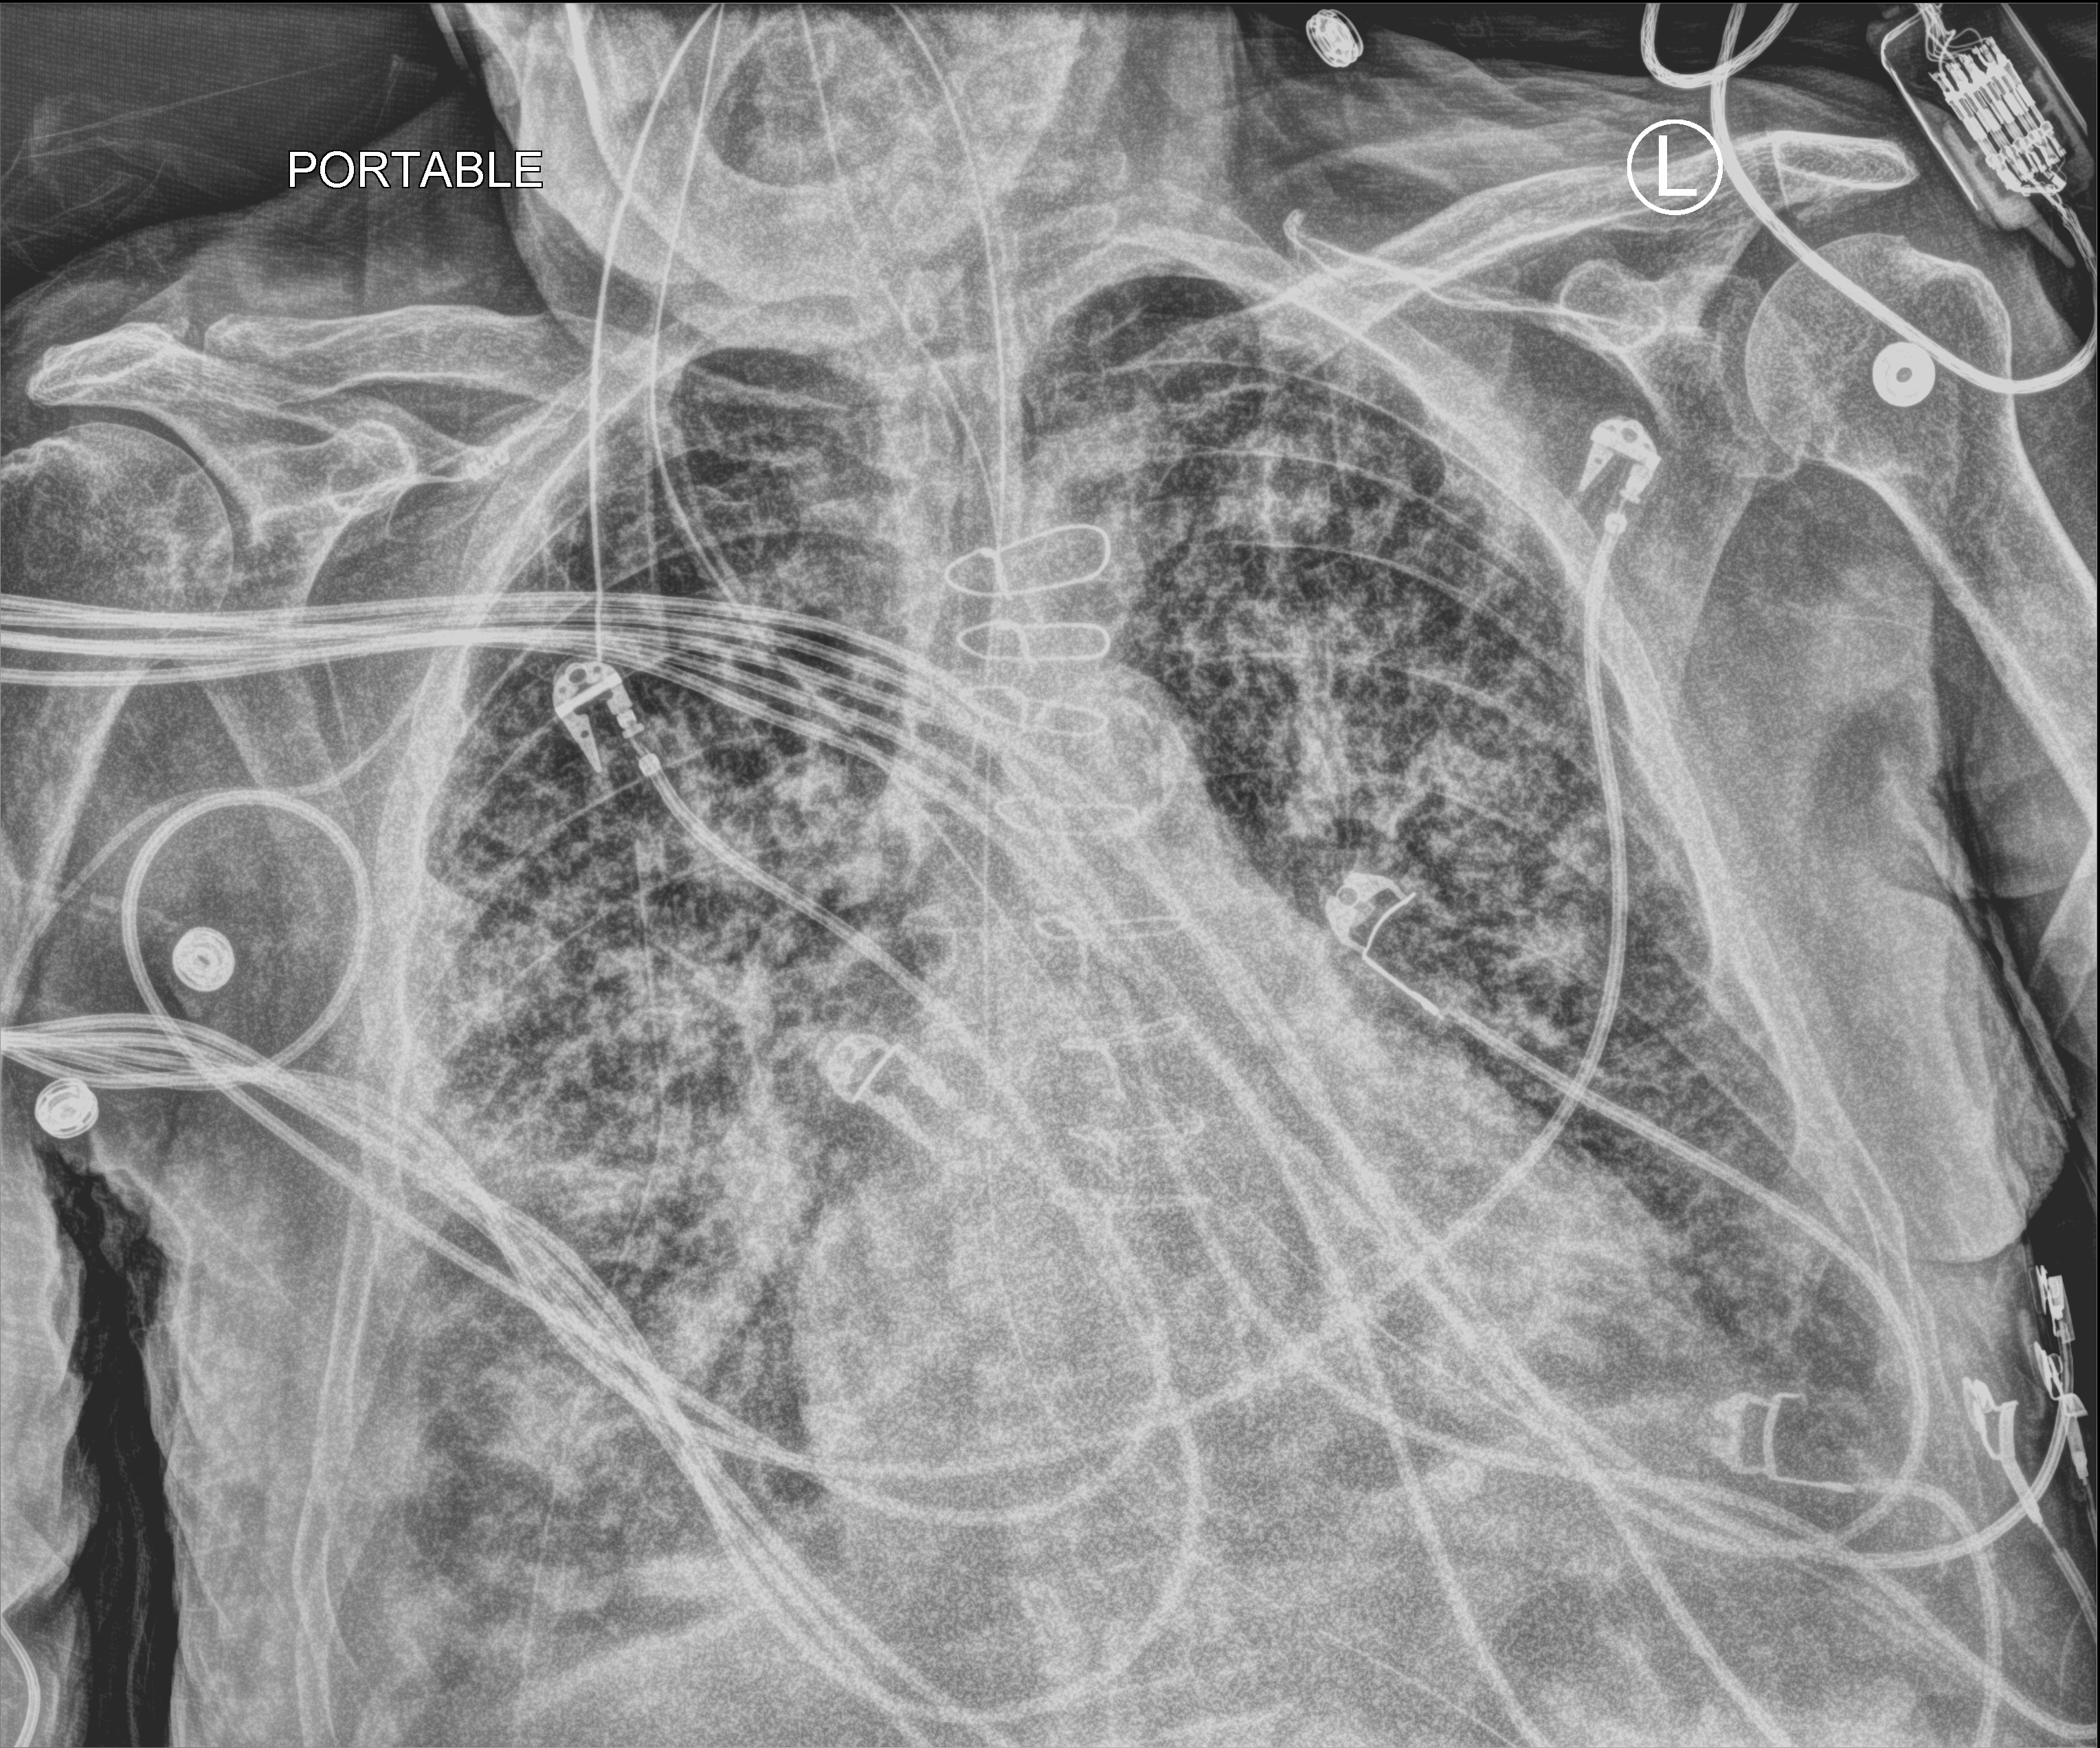
Chest X-ray (portable); anteroposterior (AP) projection. Male patient hospitalised with COVID-19, age 75–90 years.
From the hospital-stay record, not from the radiograph (when in the stay this image was taken is not recorded):
- admitted to intensive care during this hospital stay: yes